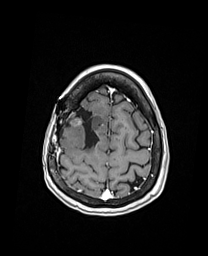
Brain MRI from a brain-tumour surgery series, one axial slice; position 40 of 192 along the scan axis; T1-weighted post-contrast; 208 × 256 image matrix, field of view 208 × 256 mm. From the clinical record (not read from this slice): histopathology: Oligodendroglioma; WHO grade: 3; IDH mutation: yes; tumour location: Right Frontal.
Annotated regions visible in this slice (expert manual segmentation):
- previous resection cavity: bounding box (x1, y1, x2, y2) in pixels: (72, 109, 99, 148)